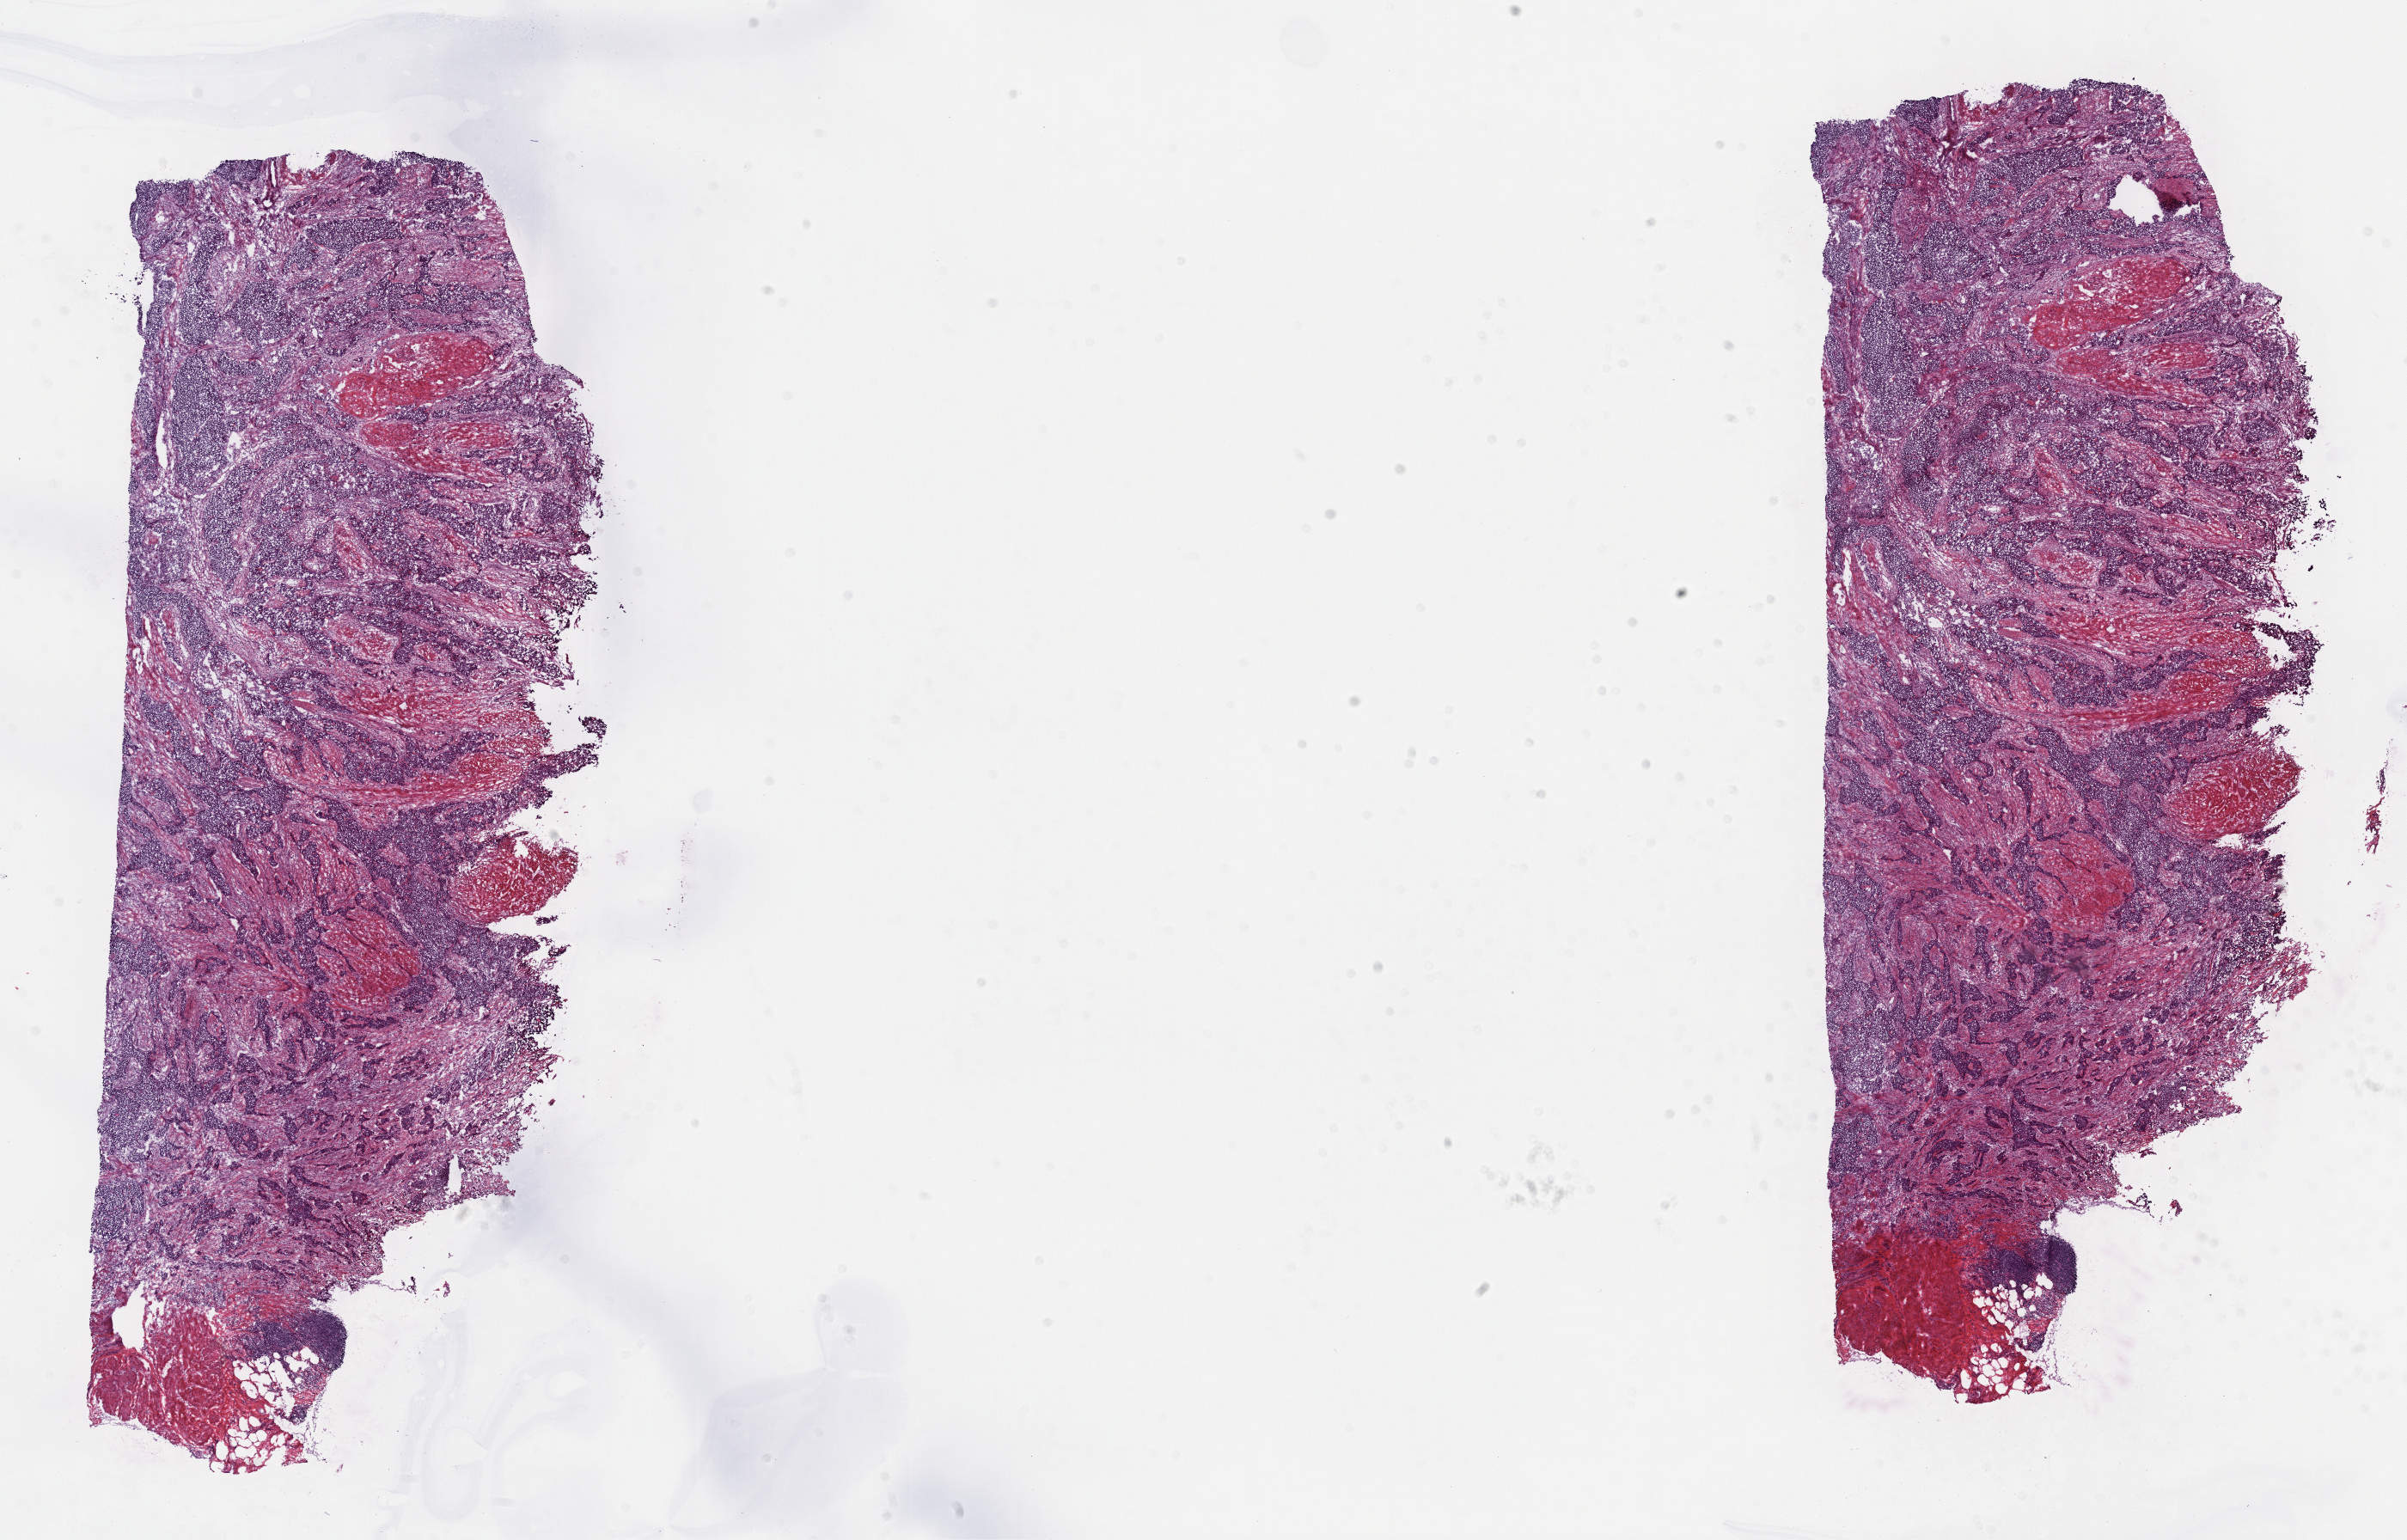
Digitized H&E tissue section (whole slide) — shown as a low-resolution overview of the whole scanned area (about 22.7 x 14.5 mm, slide scanned at 40x). Frozen section from the top of the tissue portion. Primary tumour sample from the bladder. Male, age 48 years at initial diagnosis. Histologic grade: high grade. Slide review estimates, as recorded: tumour cells 100%, tumour nuclei 65%, normal cells 0%, stromal cells 0%, necrosis 0%. Inflammatory infiltration, as recorded: lymphocyte infiltration 3%, monocyte infiltration 0%, neutrophil infiltration 0%.
Diagnosis: Transitional cell carcinoma (dome of bladder). Lymph nodes positive (case pathology): 1 of 18 examined. AJCC pathologic stage: IV (7th edition).